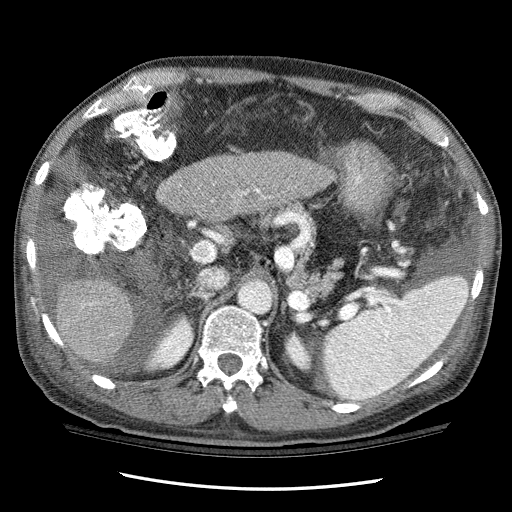
Contrast-enhanced abdominal CT (liver protocol), one axial slice. 120 kVp. One of 3 acquisitions stored at this slice position. Soft-tissue window (W 400 / L 40 HU). 2.5 mm slice thickness. 512 × 512 image matrix, field of view 360 × 360 mm. Case-level facts recorded for this patient, not image findings: diagnosis: hepatocellular carcinoma (patient treated with transarterial chemoembolisation; whether this scan precedes or follows treatment is not stated here); TNM stage (as recorded): Stage-I; Child-Pugh class: C.
Structures marked on this image (semi-automatic segmentation, software-assisted and operator-edited):
- liver parenchyma outside the tumour (the mass and vessels are separate outlines, so this box may not span the whole liver): bounding box (x1, y1, x2, y2) in pixels: (56, 152, 332, 364)
- liver vessels: (90, 189, 260, 306)